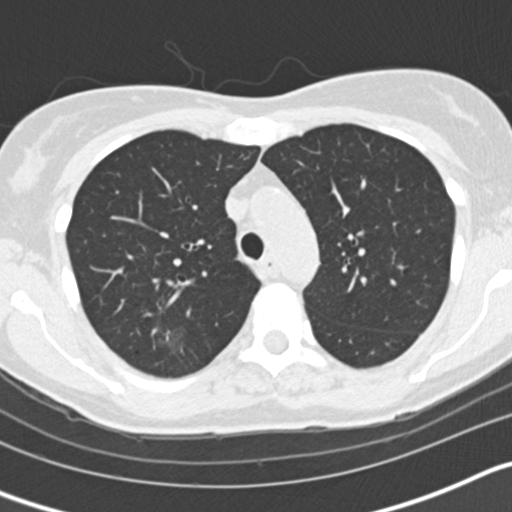
Low-dose screening chest CT, one axial slice; slice 116 of 163 in the series (ordered by position); reconstruction kernel B30f; 120 kVp; lung window (W 1500 / L -600 HU); 2 mm slice thickness; 512 × 512 image matrix, field of view 300 × 300 mm.
Structures marked on this image (expert manual segmentation):
- lesion 1 (tumor, upper lobe of right lung): box from (x=166, y=331) to (x=170, y=341) px